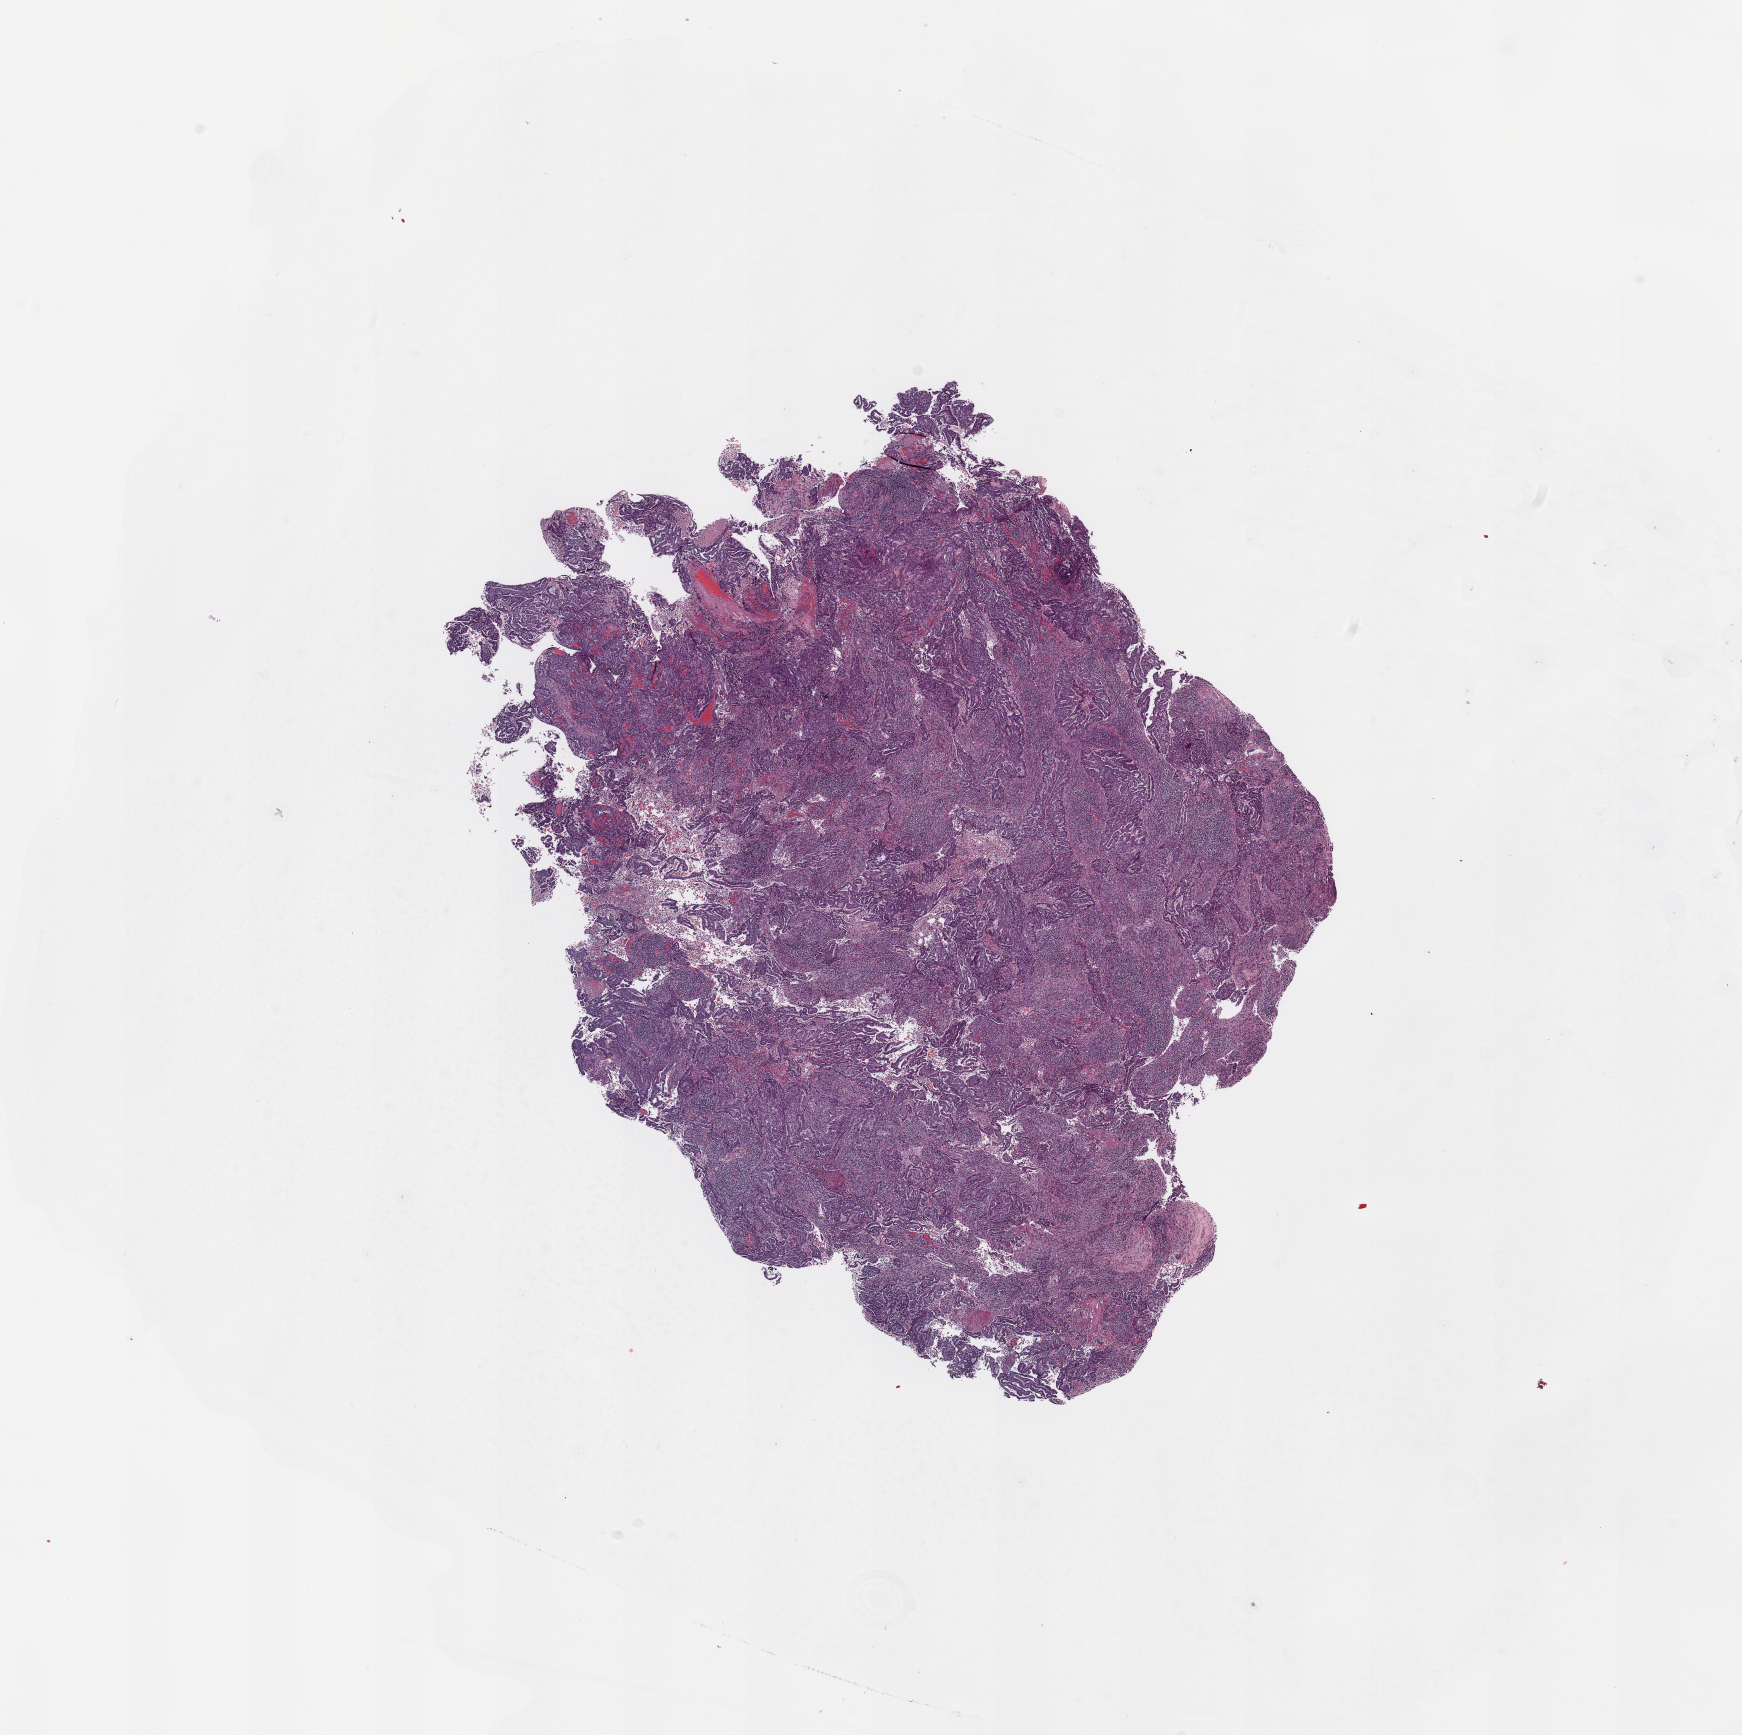
Digitized H&E tissue section (whole slide) — whole scanned area (about 13.8 x 13.7 mm) shown as a low-resolution overview; tumour tissue sample, uterus. Patient: female, age 48 years. Histologic grade: G3 (poorly differentiated).
Histologic diagnosis: Endometrioid adenocarcinoma, NOS. AJCC pathologic stage: II.